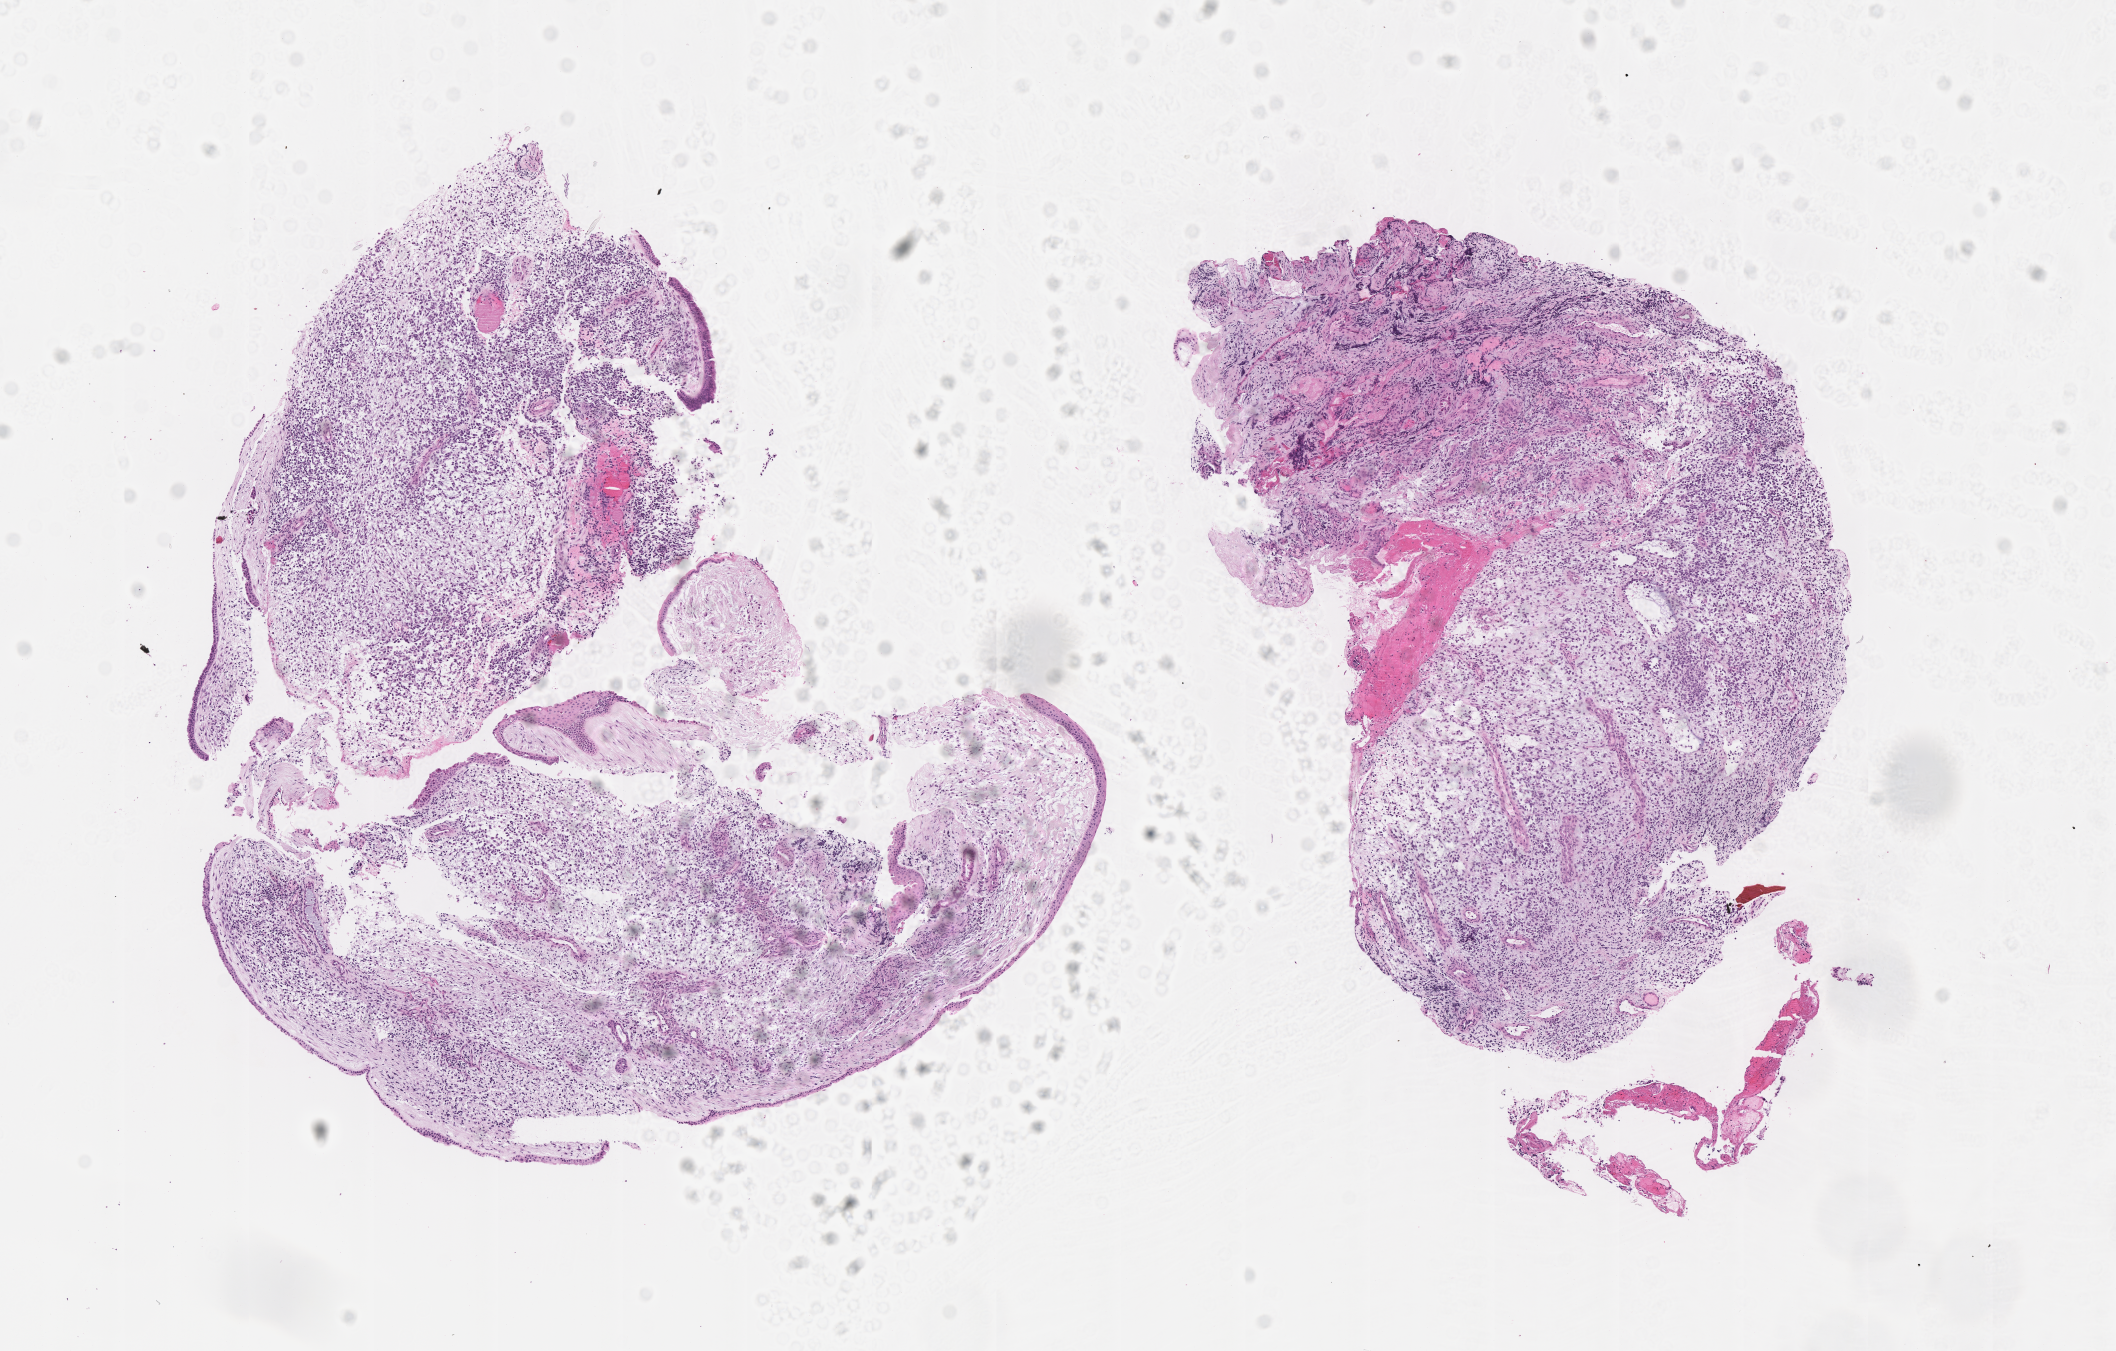
Whole-slide image, haematoxylin and eosin stain of tumor tissue — shown as a low-resolution overview of the whole scanned area (about 8.6 x 5.5 mm), FFPE section, sample anatomic site: nasopharynx-right. Patient: male, age 1.7 years at diagnosis.
- stage (as recorded): 3
- diagnosis: rhabdomyosarcoma; histological classification: embryonal rhabdomyosarcoma
- primary site (case record): nasopharynx (PM)
- metastatic status at presentation (as recorded): non-metastatic (unconfirmed)